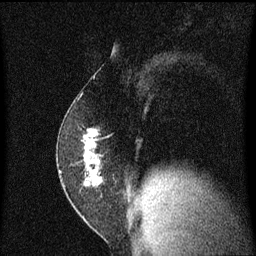
Breast MRI (dynamic contrast-enhanced), one sagittal slice; slice 35 of 60 in the series (ordered by position); dynamic contrast-enhanced series, image 2 of 3 at this slice position (ordered by acquisition); 1.5 T; TE 4.2 ms, TR 8.4 ms; 2 mm slice thickness; 256 × 256 image matrix, field of view 200 × 200 mm. Female patient, age 52 years. From the clinical record (not read from this slice): setting: breast cancer imaged before/during neoadjuvant chemotherapy; receptor status: HER2-positive.
Structures marked on this image (semi-automatic segmentation, software-assisted and operator-edited):
- analysis volume of interest (the breast-tissue region the enhancement analysis was run in; not a lesion): box from (x=58, y=124) to (x=111, y=191) px
- tumour enhancement mask (voxels above the 70 % enhancement threshold inside the analysis volume of interest): (x=84, y=128)–(x=100, y=185)